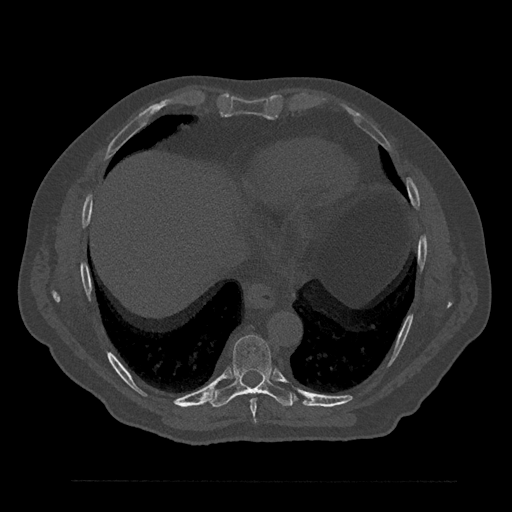
CT including the spine, one axial slice. Slice 417 of 797 in the series (ordered by position). 120 kVp. Bone window (W 1800 / L 400 HU). 0.5 mm slice thickness. 512 × 512 image matrix. Male patient, age 61 years. From the clinical record (not read from this slice): primary cancer: prostate.
Annotated regions visible in this slice (semi-automatic segmentation, software-assisted and operator-edited):
- T8 vertebra: bounding box [x1, y1, x2, y2] px = [250, 398, 257, 424]
- T9 vertebra: [209, 335, 296, 408]